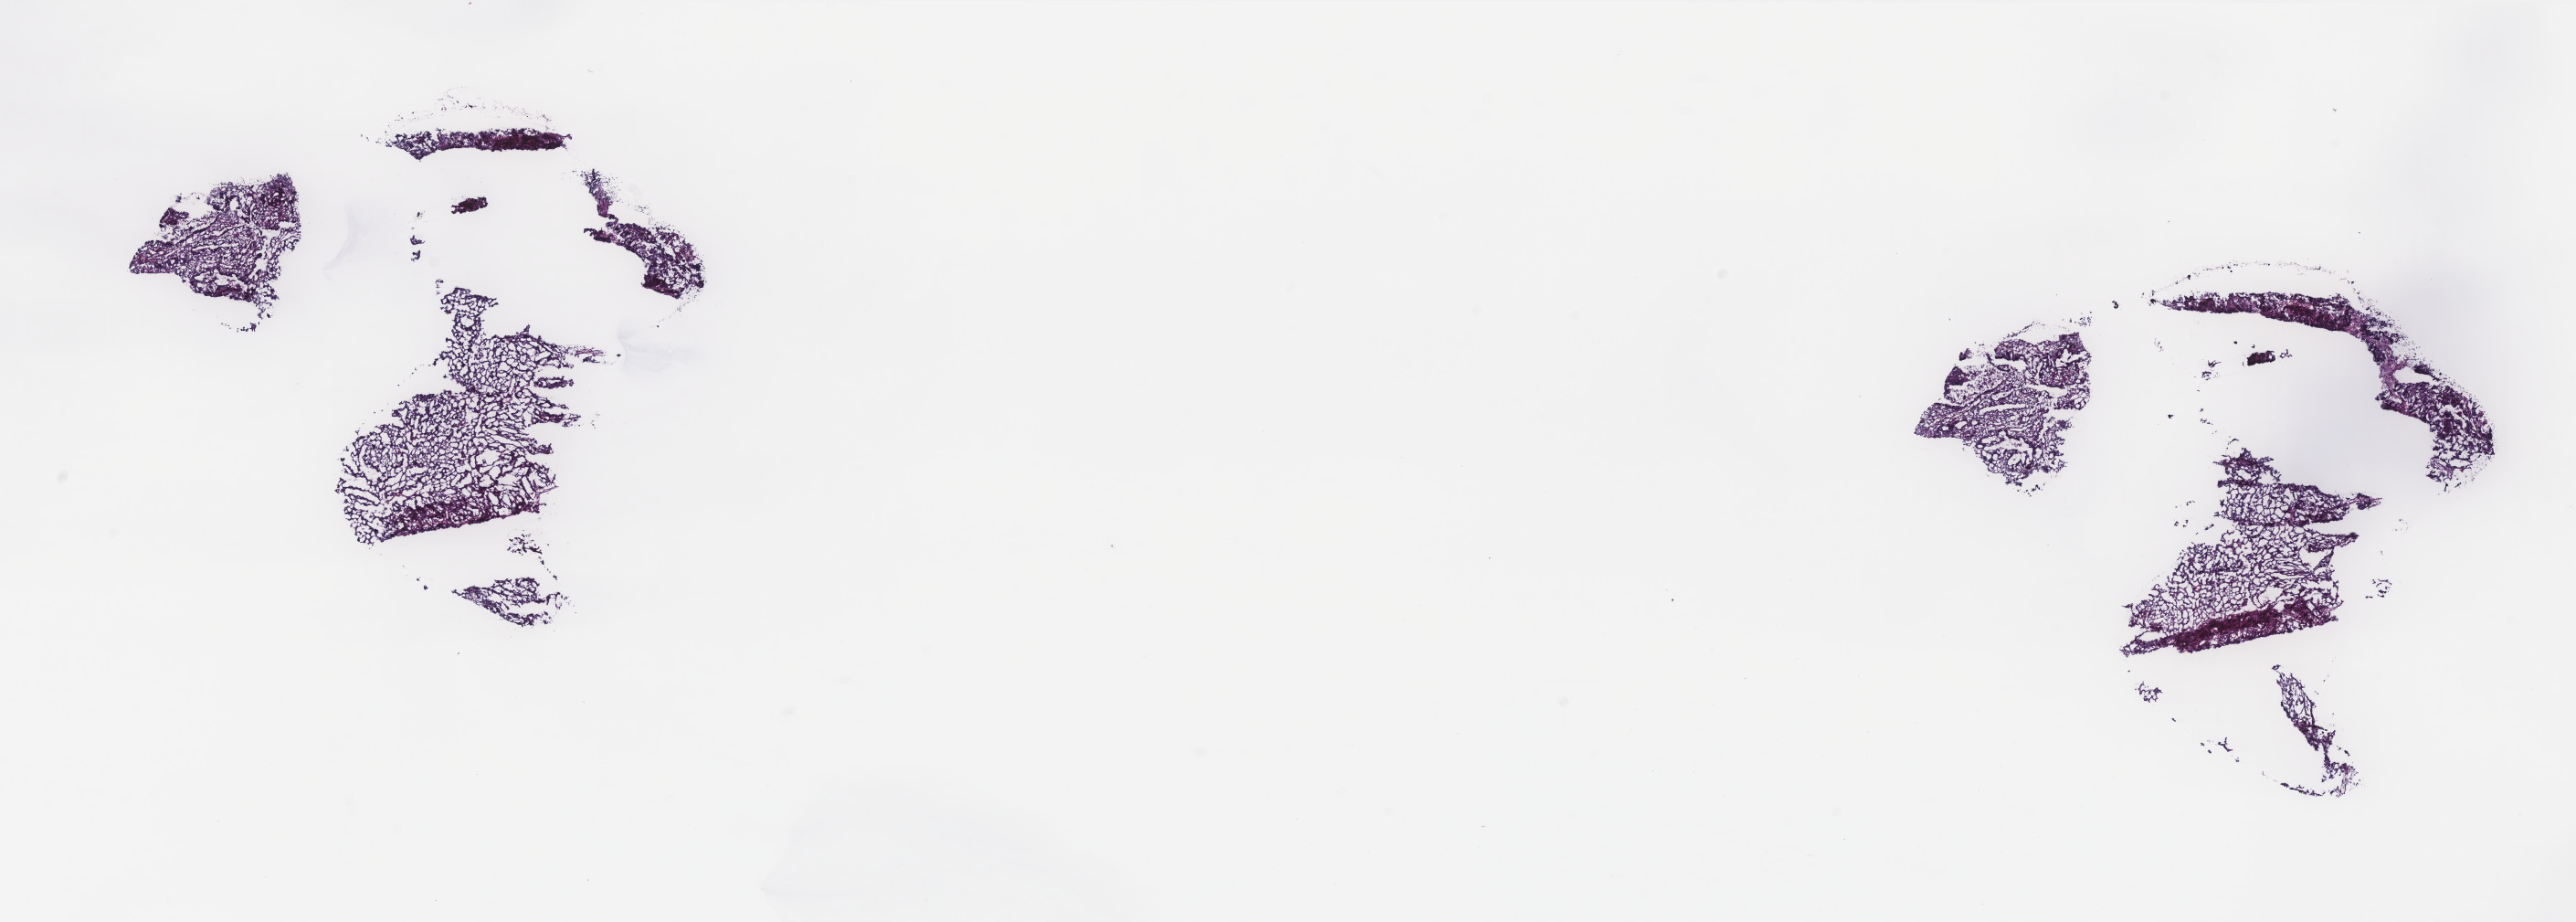
H&E-stained whole-slide image, a low-resolution overview of the entire scanned area, about 22.6 x 8.1 mm (from a 40x scan); frozen section from the top of the tissue portion; uterus, primary tumour sample. Female patient; age at initial diagnosis 40 years. Histologic grade: G3 (poorly differentiated). Composition of this section per pathologist review: tumour cells 100%, tumour nuclei 75%, normal cells 0%, stromal cells 0%, necrosis 0%. Inflammatory infiltration, as recorded: lymphocyte infiltration 0%, monocyte infiltration 0%, neutrophil infiltration 0%.
FIGO stage: IB. Diagnosis: Endometrioid adenocarcinoma, NOS (endometrium).